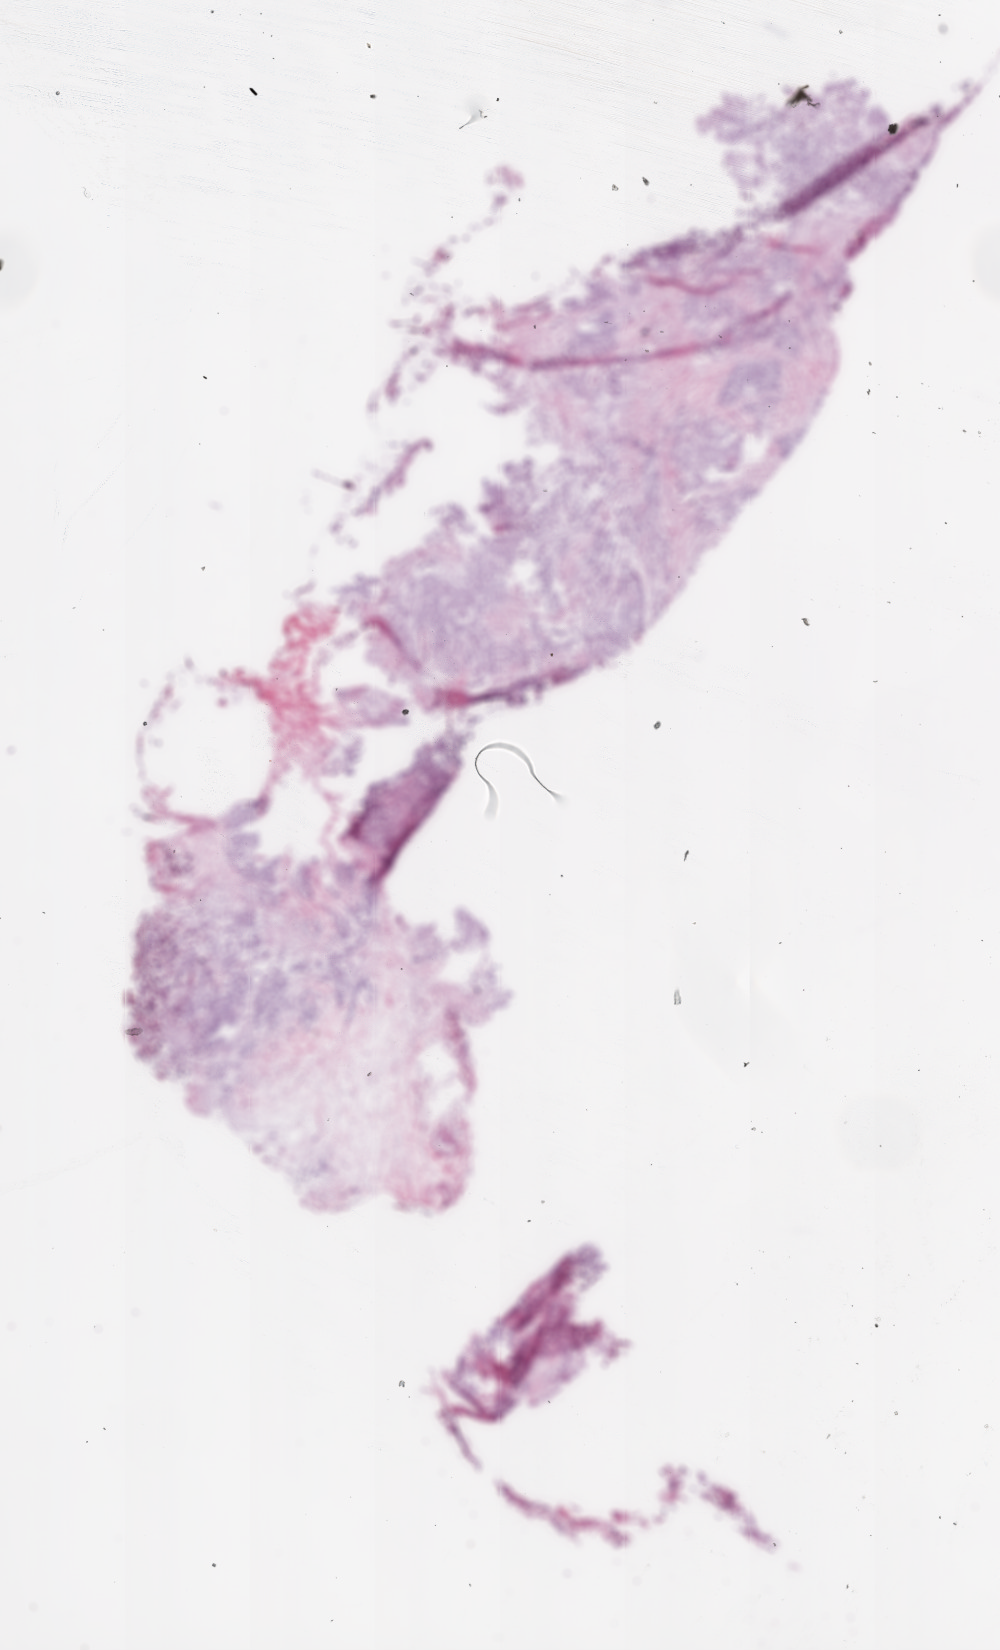
Whole-slide histology image, H&E-stained, whole scanned area (about 8.0 x 13.2 mm, acquisition: 20x scan) shown as a low-resolution overview, frozen section from the bottom of the tissue portion, ovary, recurrent tumour sample. Female patient; age at initial diagnosis 47 years.
This section: recurrent tumour. Patient diagnosis: Serous cystadenocarcinoma, NOS.